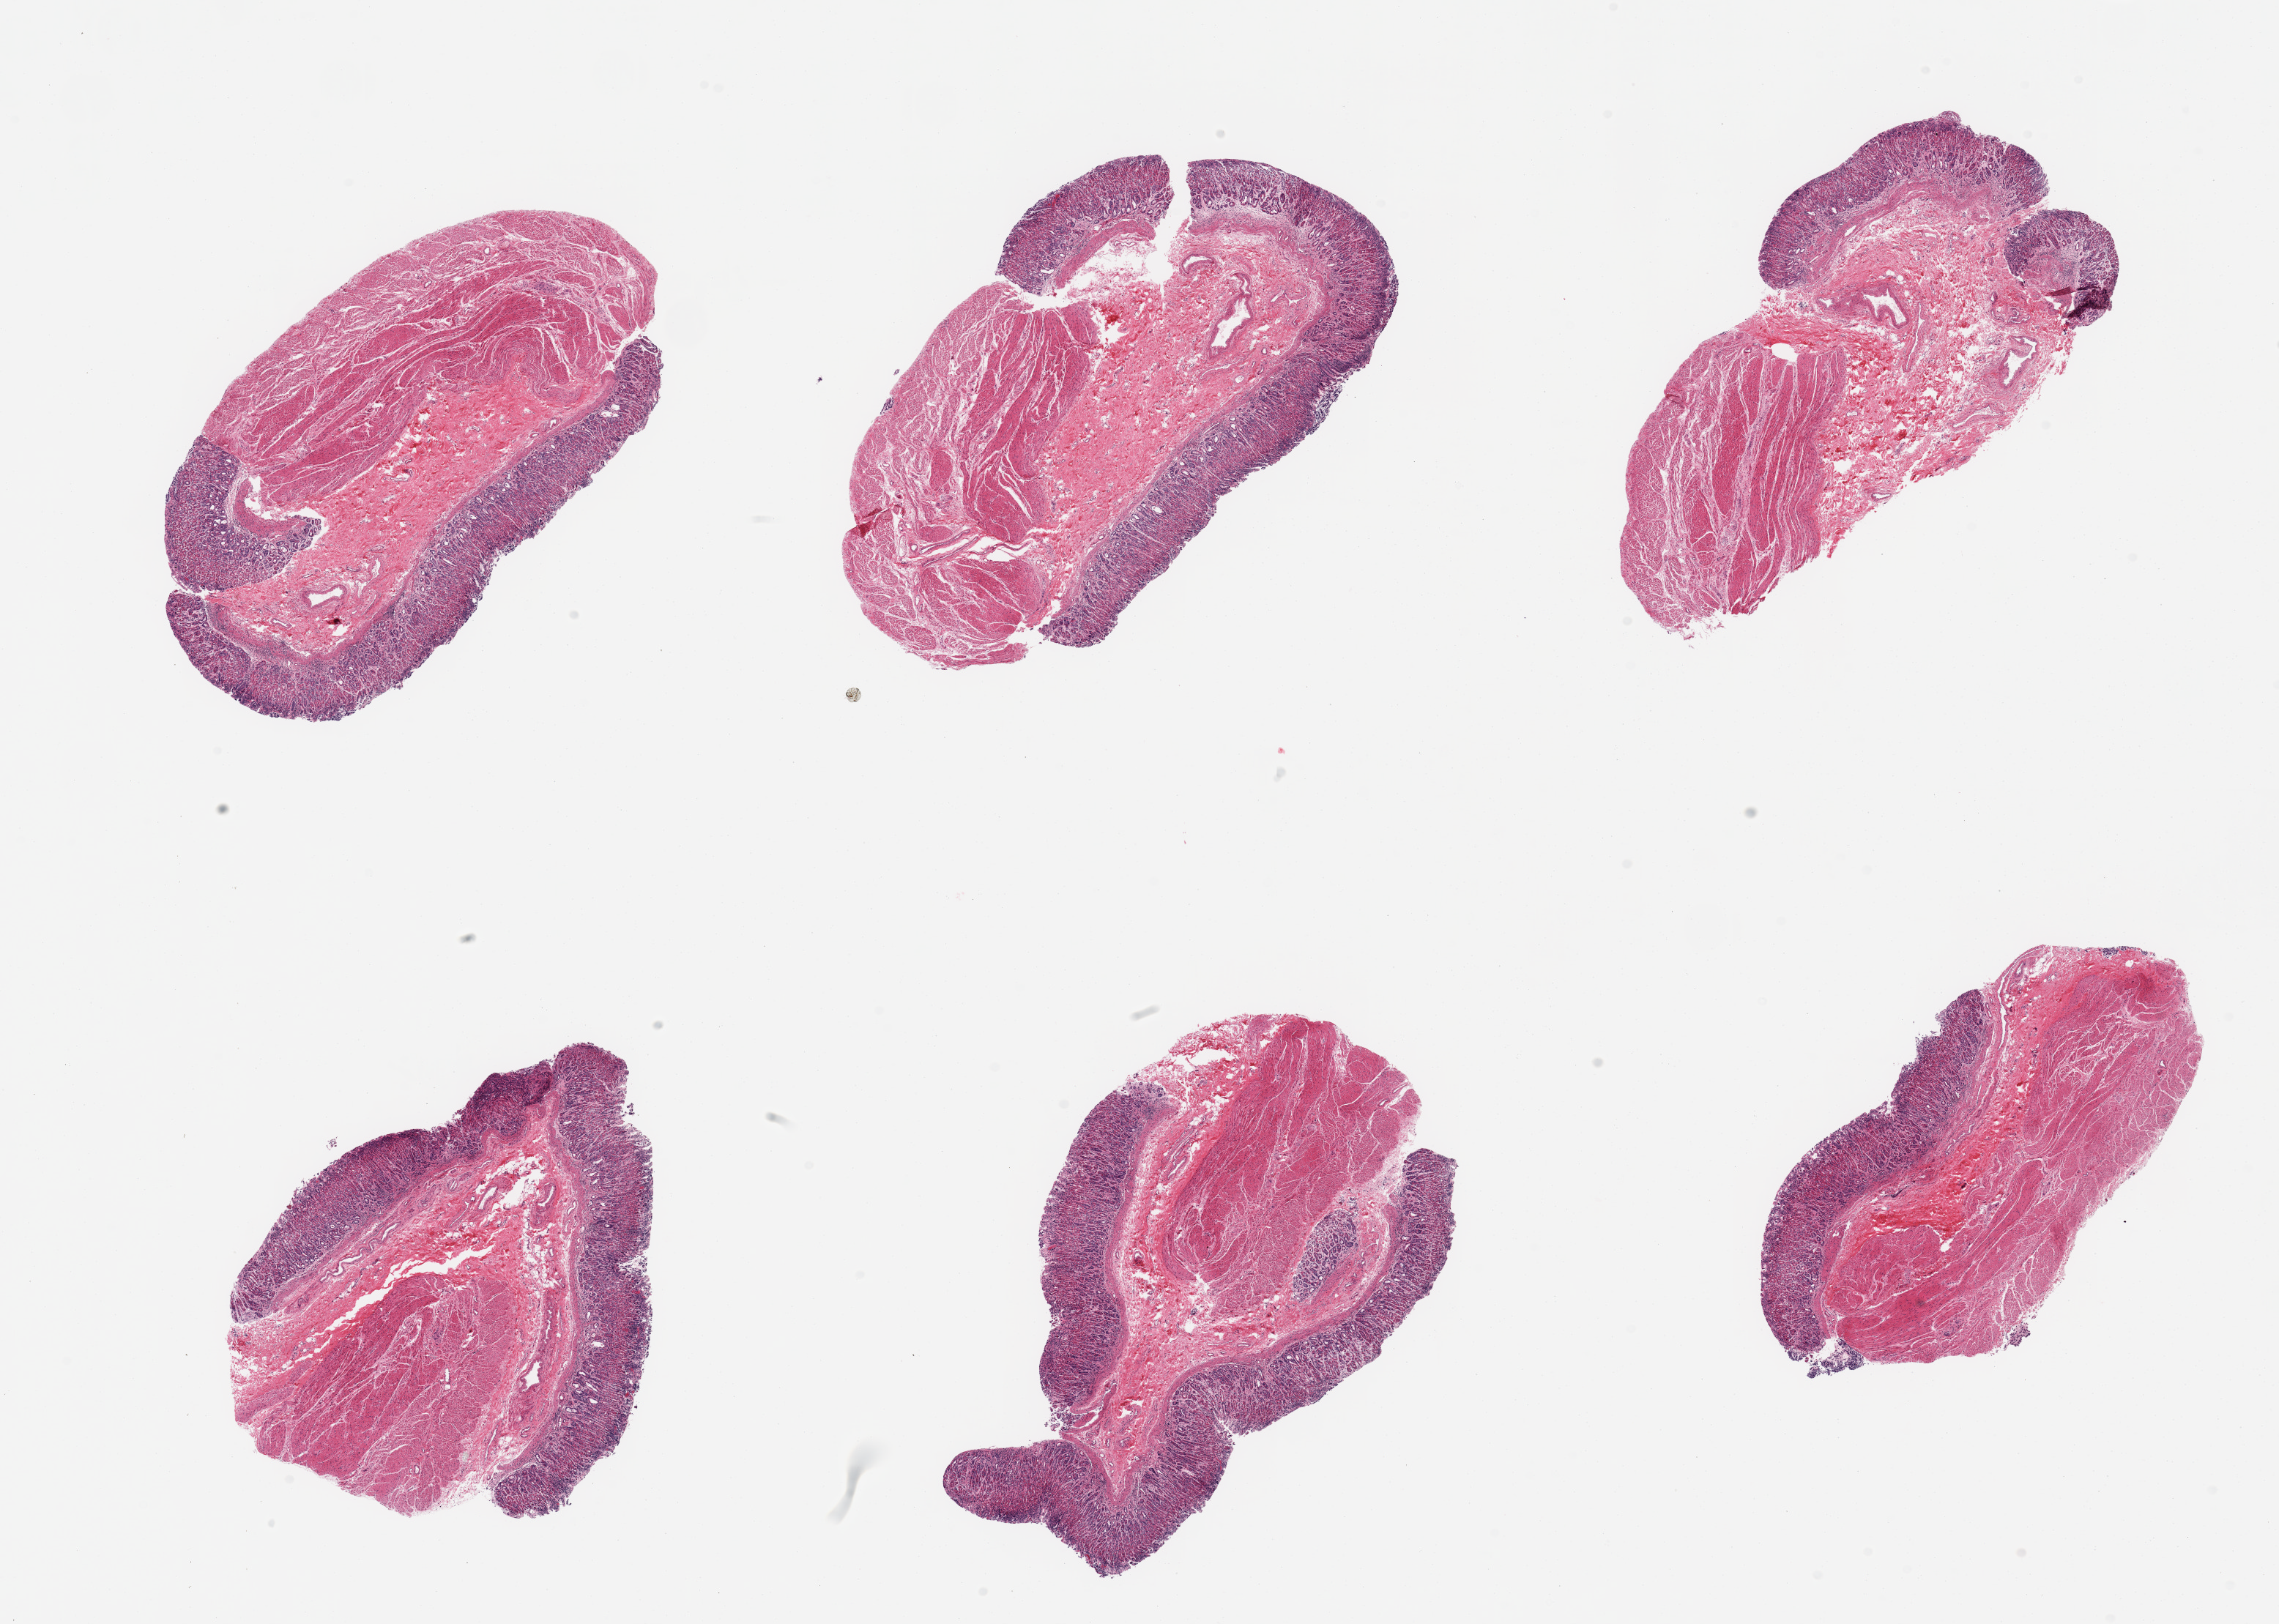
Whole-slide image, haematoxylin and eosin stain, low-resolution overview of the scanned area, about 24.6 x 17.5 mm (acquisition: 20x scan), PAXgene-fixed, paraffin-embedded tissue, target tissue: stomach, donor tissue sample. Donor: male.
* review note (as recorded): 6 pieces, superficial mucosa approached score '2', up to ~0.7mm, ~15% thickness. Chronic gastritis, microglandular cystic change noted